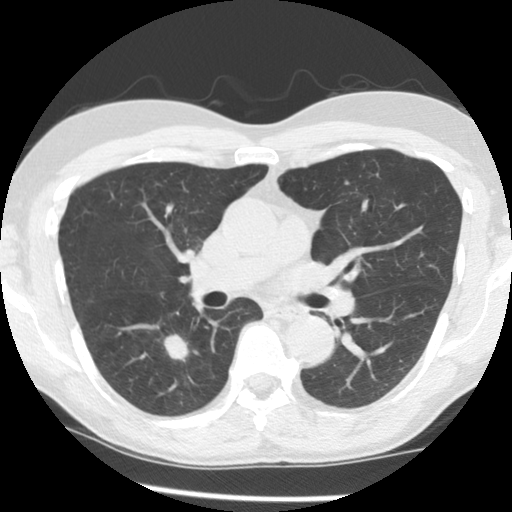
Low-dose screening chest CT, axial slice, third annual screen, lung window (W 1500 / L -600 HU), 2.5 mm slice thickness, slice 81 of 145 in the series, 512 × 512 image matrix, field of view 320 × 320 mm. Male, age 65 years at enrolment. Current smoker at enrolment.
- Expert-annotated lung lesion, bounding box <147,322,207,377> (left, top, right, bottom; pixels).
- The screening reader recorded 2 non-calcified nodules or masses ≥4 mm on this exam (left lower lobe, right lower lobe); which of them this box marks is not recorded.
- Lung cancer was diagnosed 116 days after this screen: adenocarcinoma, NOS, right lower lobe, poorly differentiated (G3), stage IA (AJCC 6th edition), 18 mm at pathology.